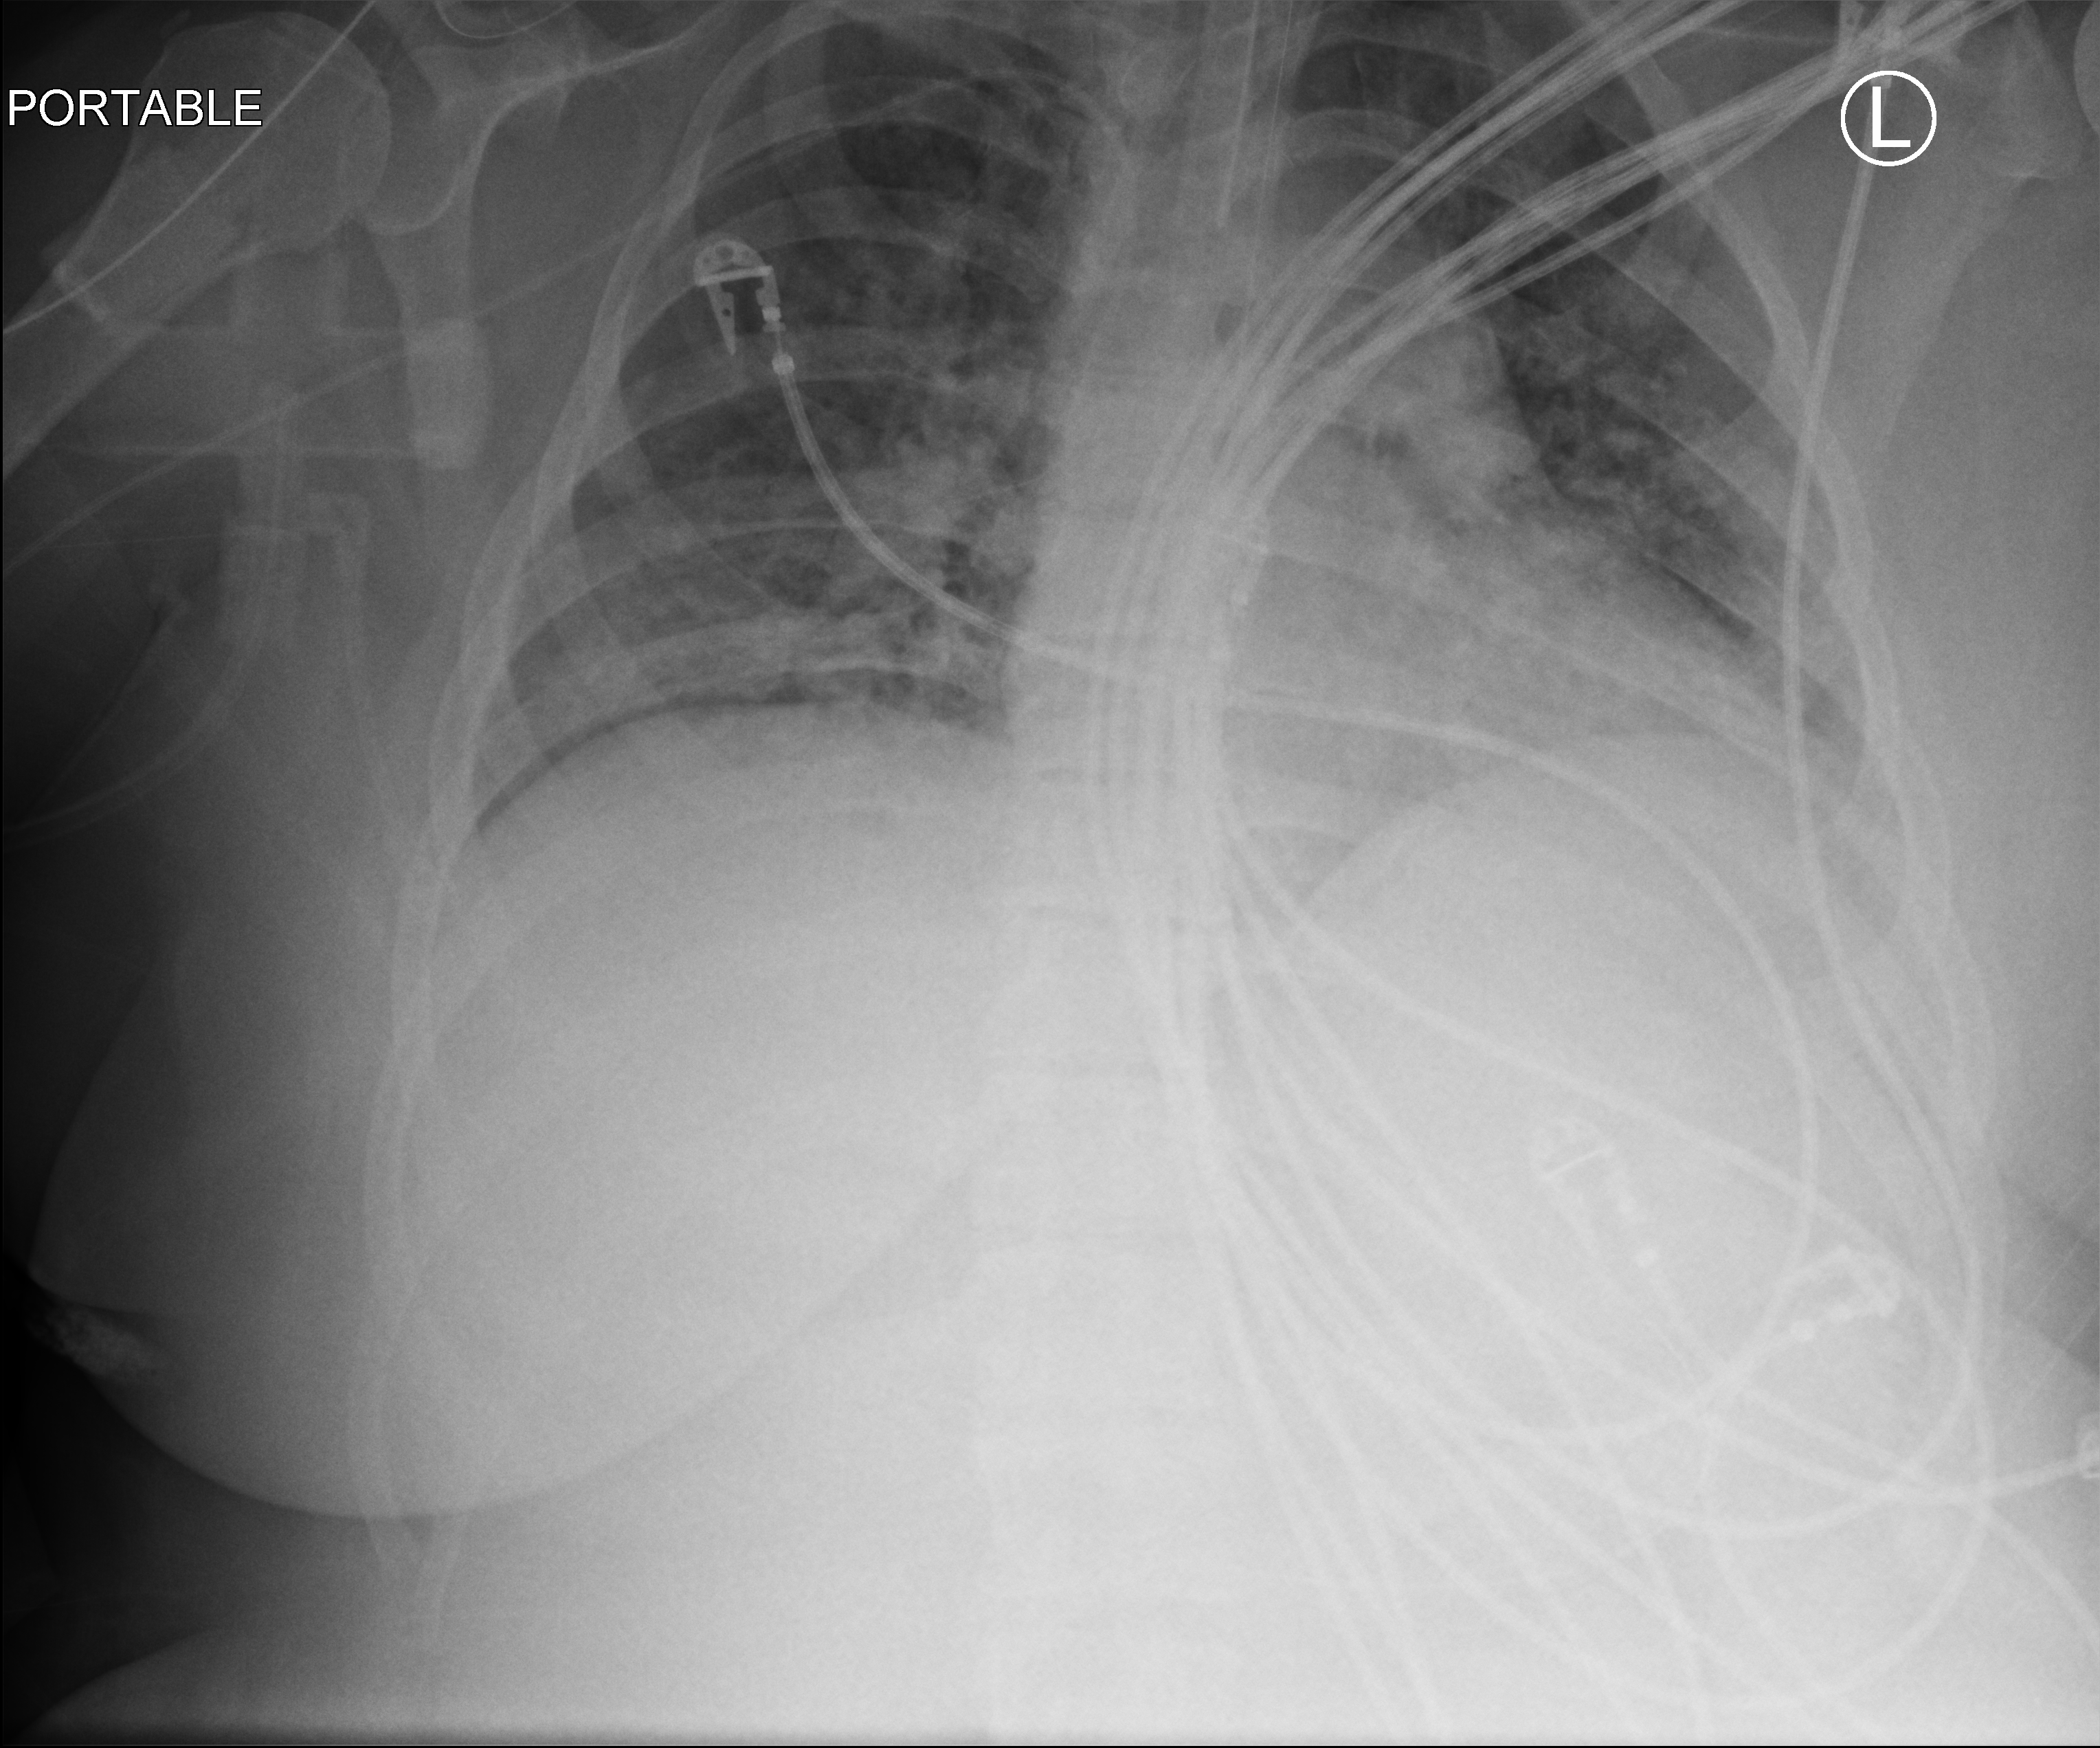
Bedside chest radiograph (computed radiography). Patient hospitalised with COVID-19; female, aged 18–59 years.
Admission-level facts for this patient (not findings on this image; timing relative to this image not recorded): admitted to intensive care during this hospital stay: yes; length of hospital stay: 25 days.